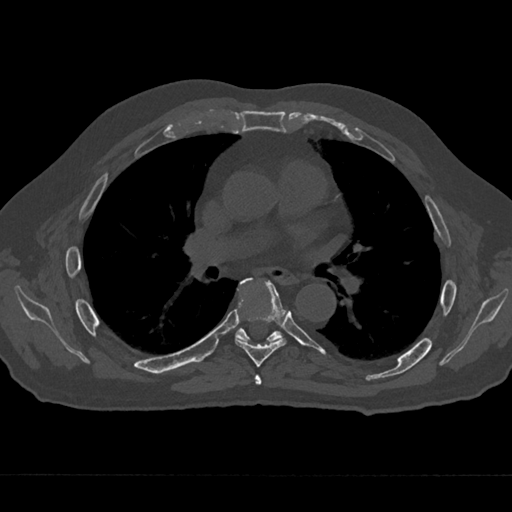
CT including the spine, one axial slice; slice 404 of 797 in the series (ordered by position); reconstruction kernel Br40s/3; bone window (W 1800 / L 400 HU); 0.5 mm slice thickness; 512 × 512 image matrix, field of view 377 × 377 mm. Patient: male, 75 years. From the clinical record (not read from this slice): primary cancer: renal; vertebrae with lytic lesions (as recorded): T4.
Structures marked on this image (semi-automatic segmentation, software-assisted and operator-edited):
- T5 vertebra: box from (x=255, y=375) to (x=262, y=385) px
- T6 vertebra: (x=235, y=278)–(x=287, y=367)
- T7 vertebra: (x=235, y=279)–(x=282, y=342)